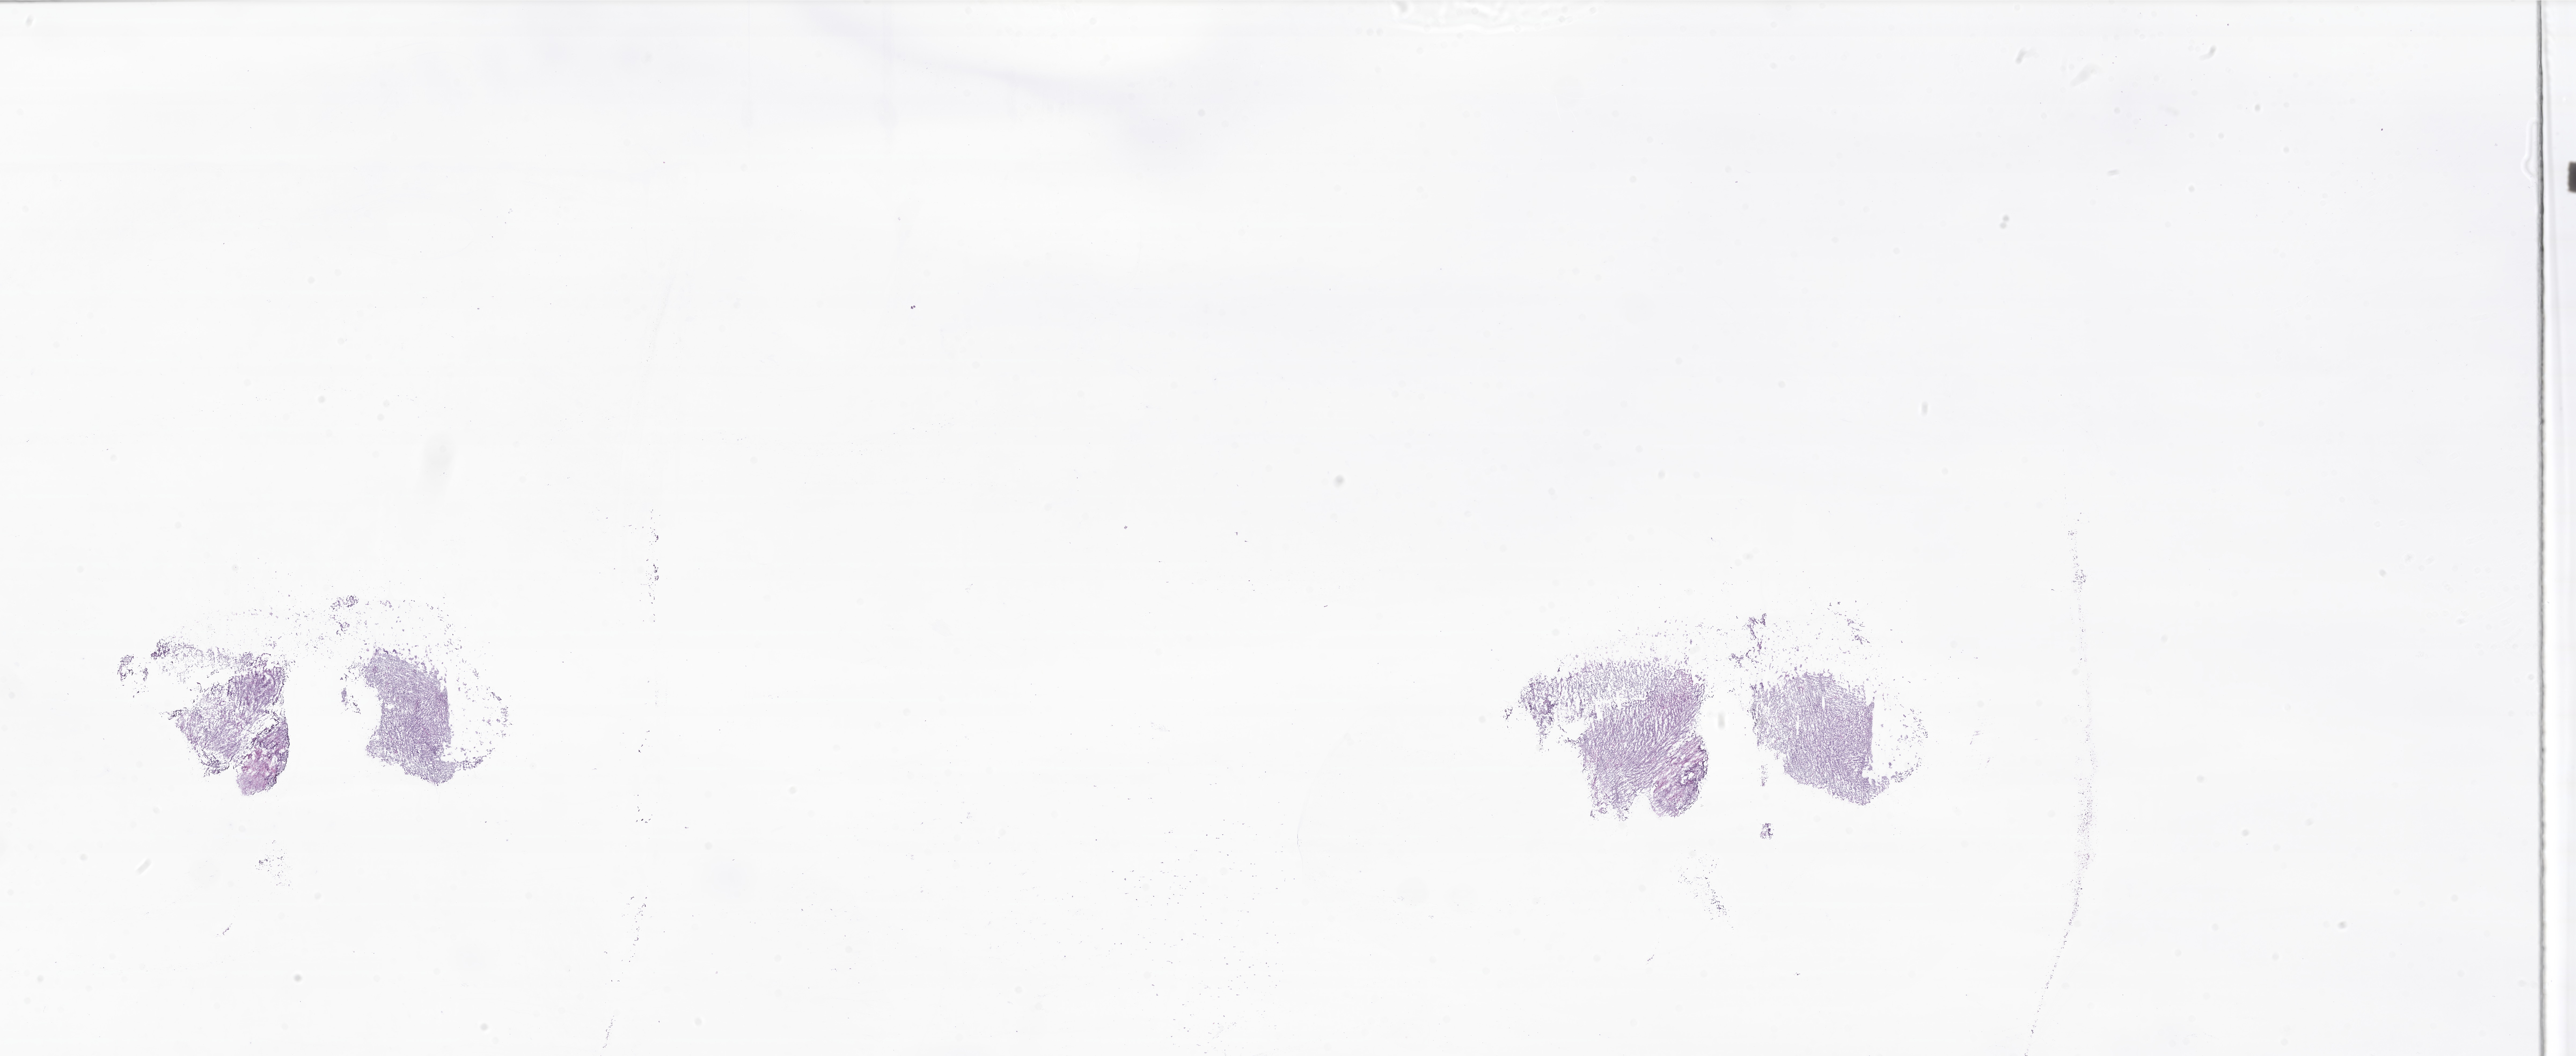
Digitized H&E-stained section of tumor tissue from the brain, shown as a low-resolution overview of the whole scanned area (about 40.5 x 16.6 mm); frozen section. Patient male; age 138 months.
Diagnosis: Medulloblastoma, NOS.